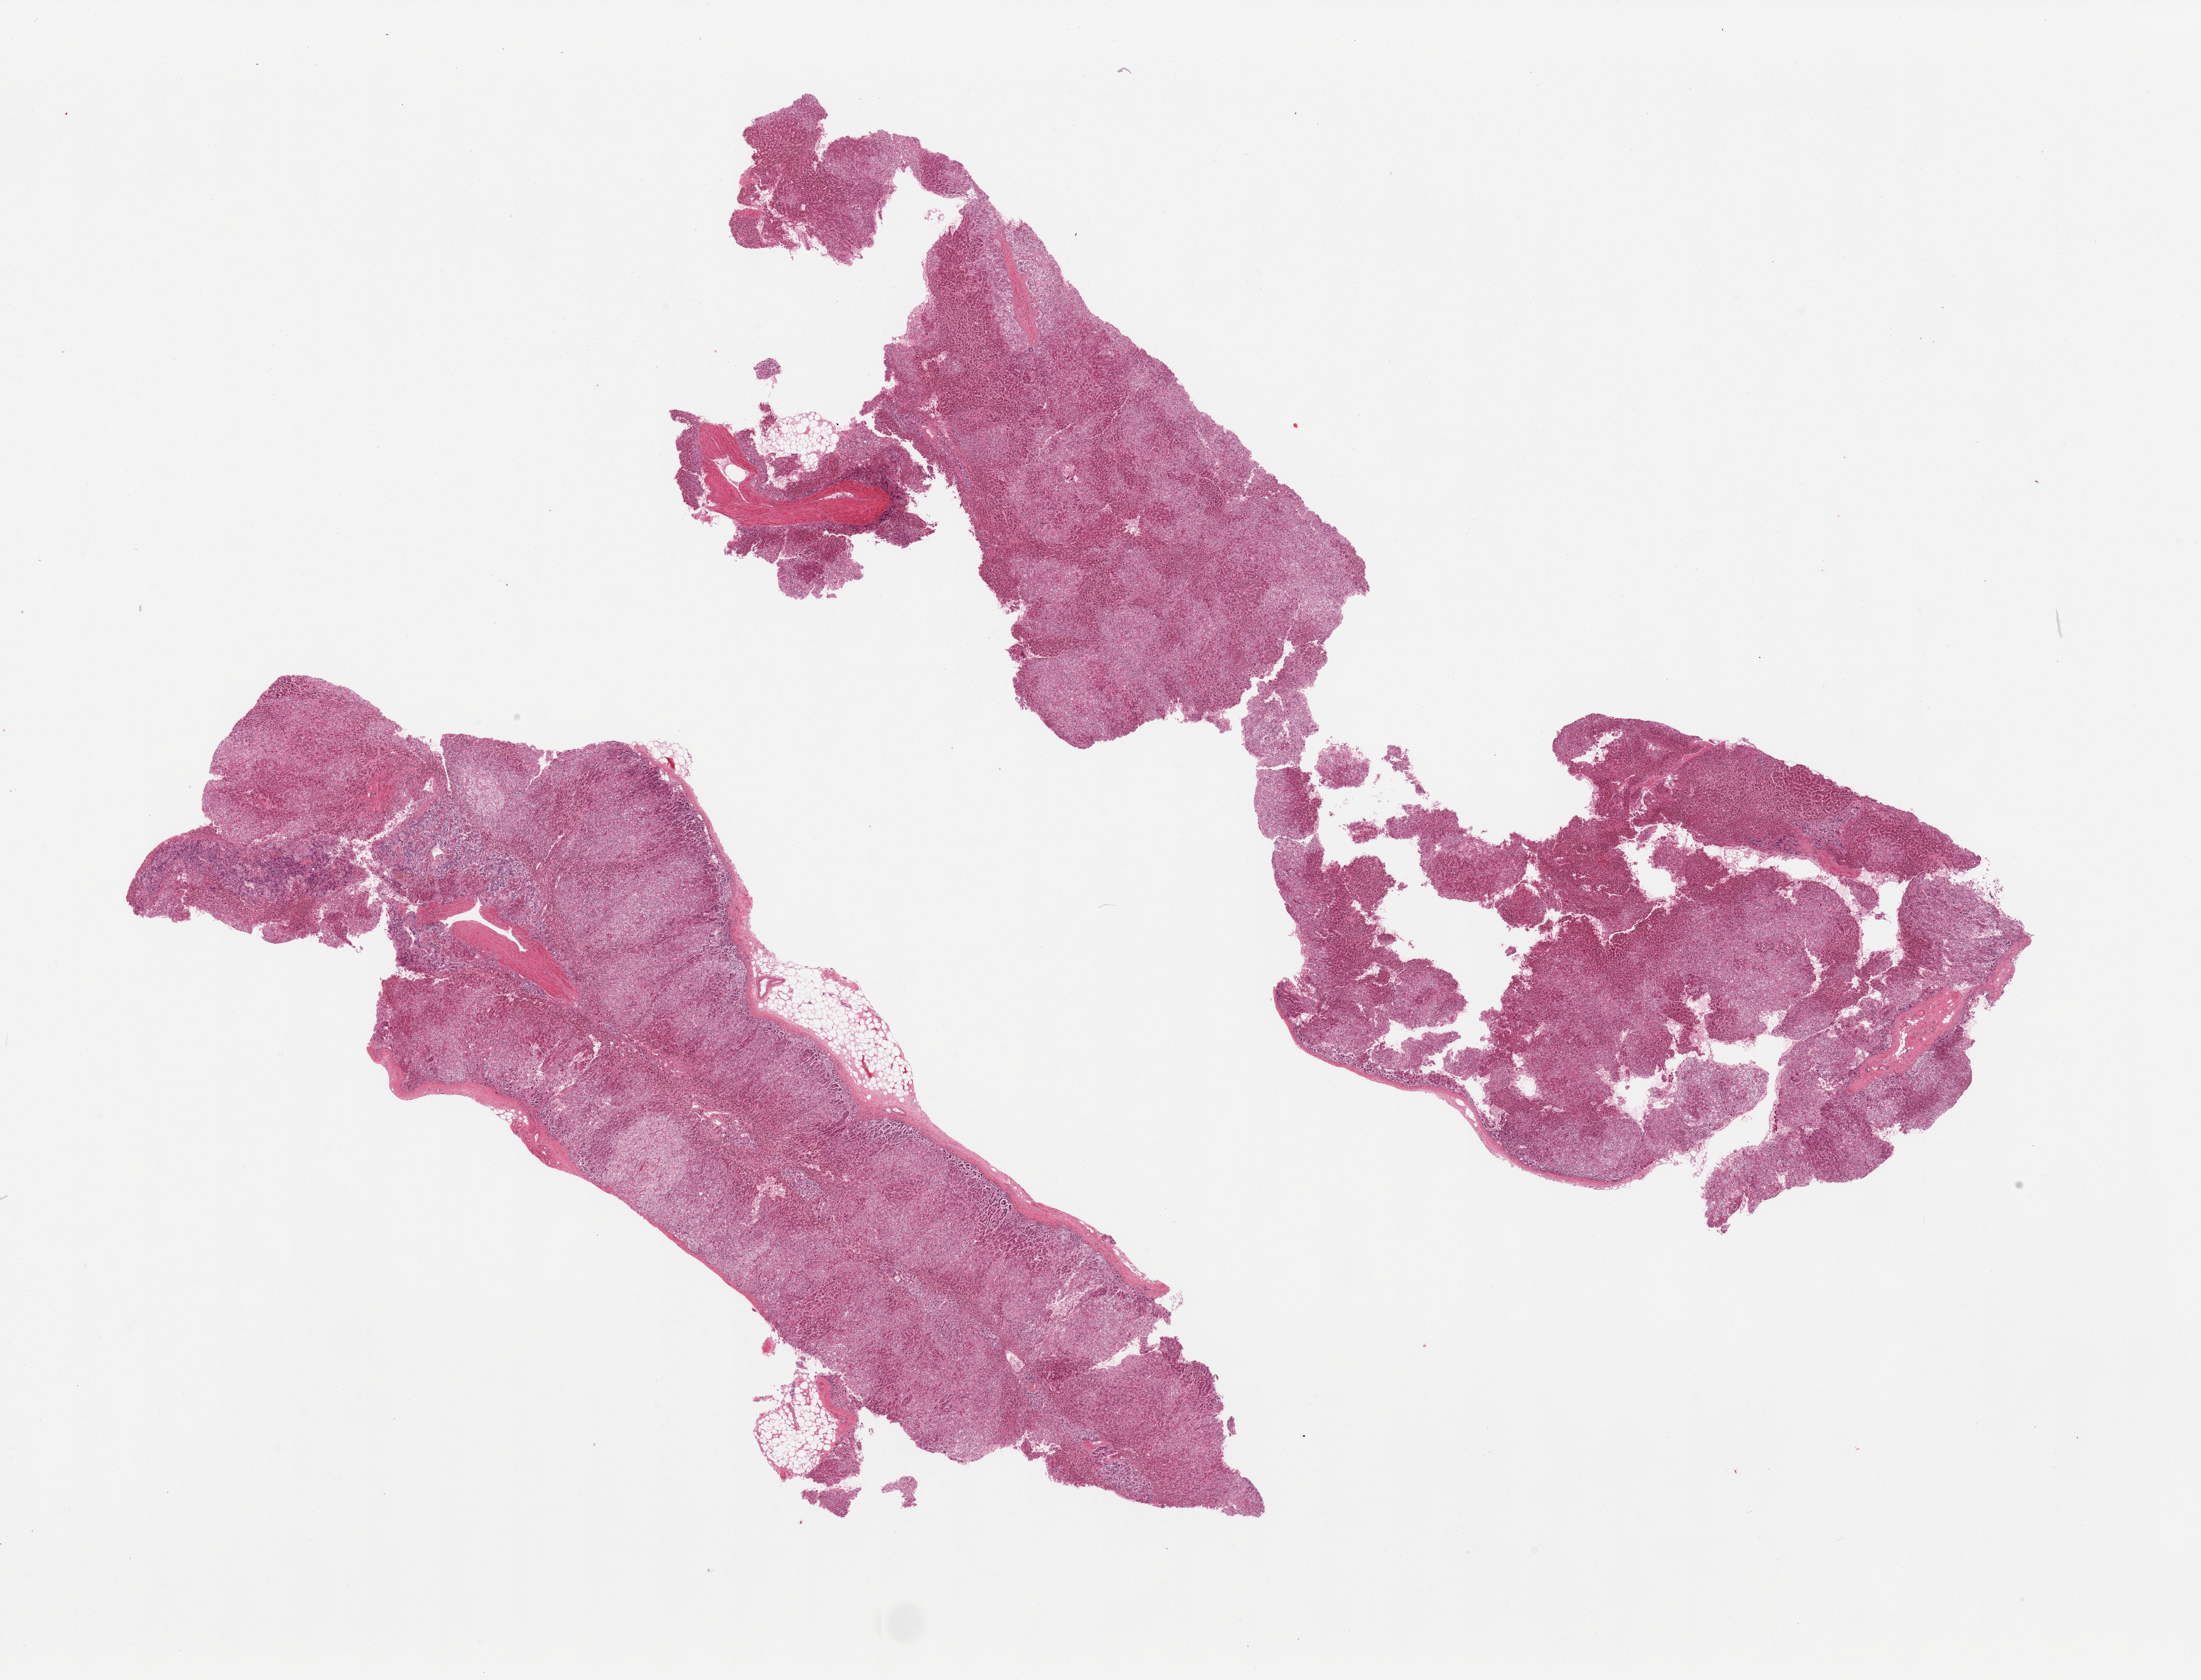
Whole-slide image, haematoxylin and eosin stain, shown as a low-resolution overview of the whole scanned area (about 29.5 x 22.5 mm), PAXgene-fixed paraffin-embedded (PFPE) section, sampled site (target tissue): adrenal gland, donor tissue sample. Male donor.
* reviewer comment on this tissue sample: 2 pieces, moderate marked autolysis, all cortex, focal nubbin 0.5mm fat adherent to one